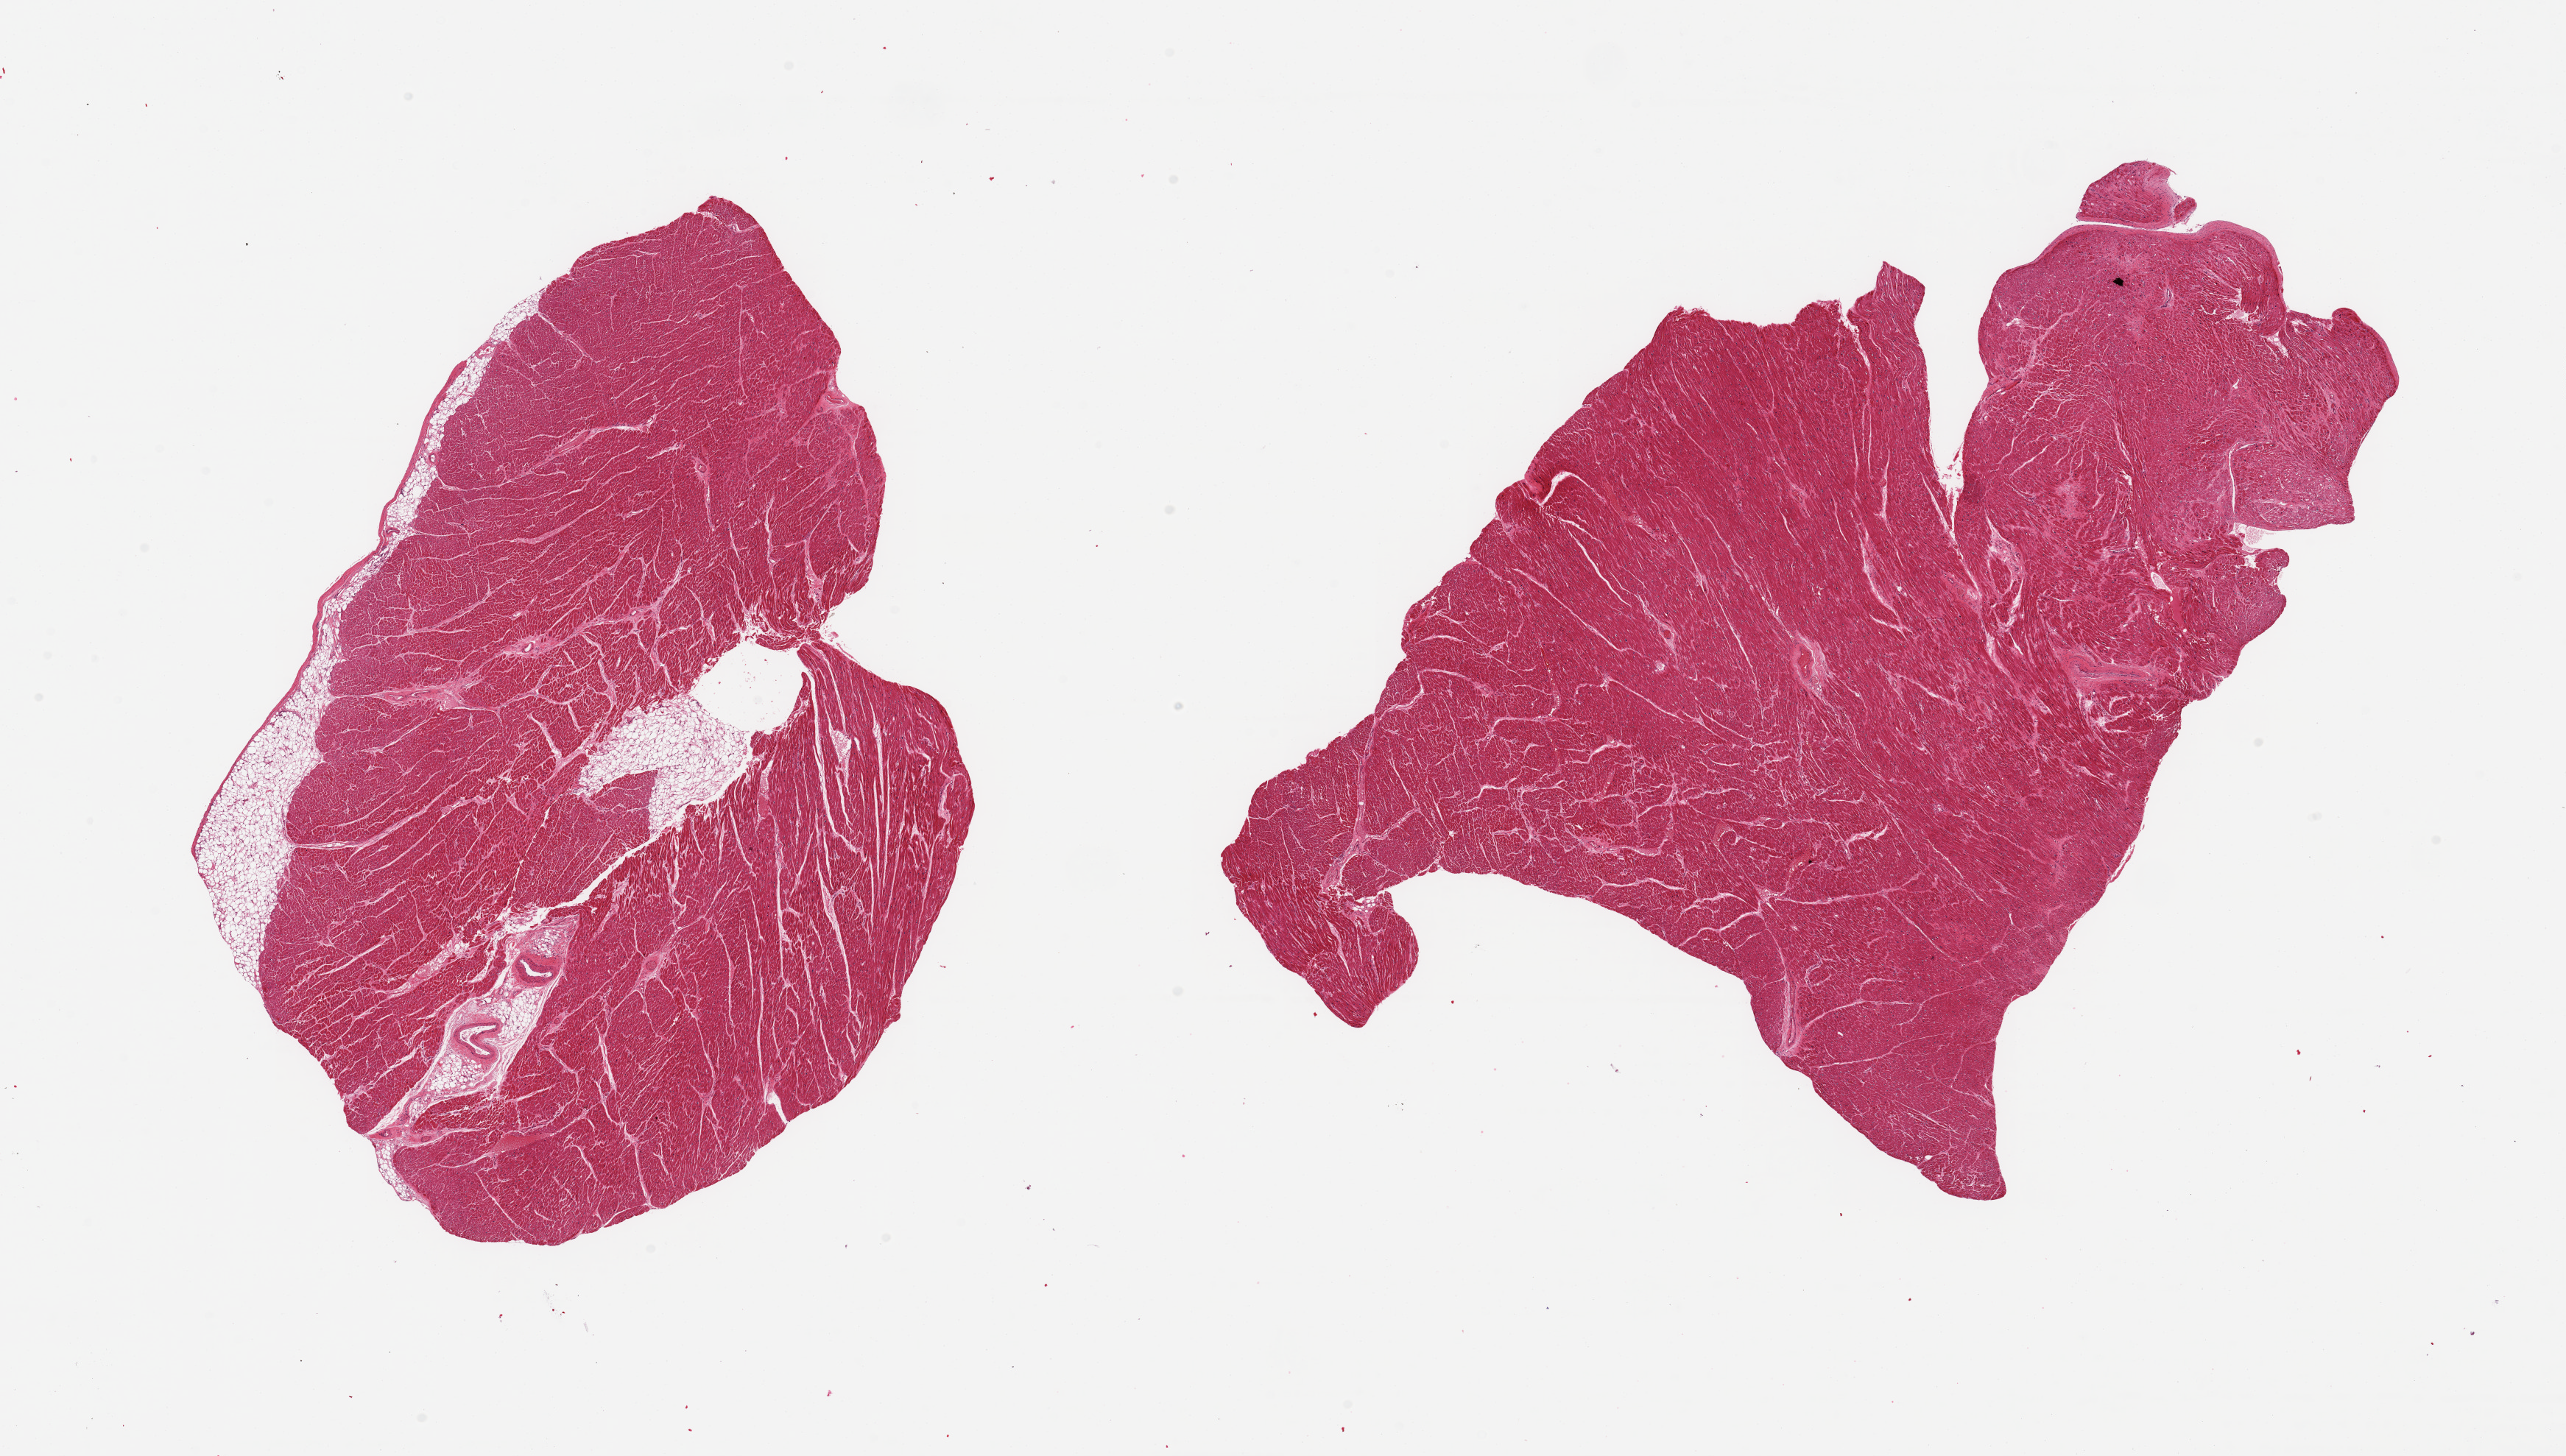
Digitized H&E-stained section, low-resolution overview of the scanned area, about 27.6 x 15.6 mm. PAXgene-fixed paraffin-embedded (PFPE) section. Sampled site (target tissue): heart. Tissue donor sample. Donor sex: male.
Reviewer comment on this tissue sample: 2 pieces; focal mild interstitial fibrosis enlarged nuclei; 1 piece has 10% internal & external fat content.